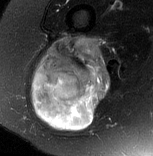
MRI of an extremity soft-tissue mass, one axial slice; position 43 of 77 along the scan axis; T2-weighted fat-saturated; MR volume resampled by the dataset authors to the PET/CT grid (not the native acquisition matrix); 153 × 156 image matrix, field of view 149 × 152 mm. Female patient. Case-level facts recorded for this patient, not image findings: histological type: synovial sarcoma; grade: intermediate; site of the primary tumour: right buttock.
Structures marked on this image (expert contour drawn on MRI and transferred to this co-registered scan by the dataset authors):
- gross tumour volume including surrounding oedema: bounding box <32,36,111,130> (left, top, right, bottom; pixels)
- gross tumour volume (mass): <32,36,111,130>